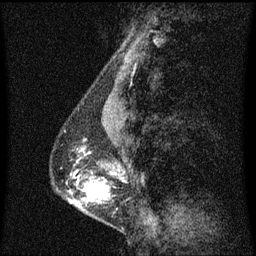
Breast MRI (dynamic contrast-enhanced), one sagittal slice; slice 23 of 60 in the series (ordered by position); dynamic contrast-enhanced series, image 2 of 3 at this slice position (ordered by acquisition); 1.5 T; TE 4.2 ms, TR 8.4 ms; 2 mm slice thickness; 256 × 256 image matrix, field of view 200 × 200 mm. Patient: female, 40 years. From the clinical record (not read from this slice): setting: breast cancer imaged before/during neoadjuvant chemotherapy; receptor status: triple-negative.
Outlined on this slice (semi-automatically segmented with operator editing):
- analysis volume of interest (the breast-tissue region the enhancement analysis was run in; not a lesion): bounding box <62,128,120,215> (left, top, right, bottom; pixels)
- tumour enhancement mask (voxels above the 70 % enhancement threshold inside the analysis volume of interest): <83,182,108,199>